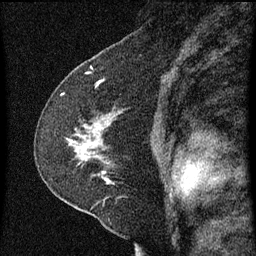
Breast MRI (dynamic contrast-enhanced), one sagittal slice. Slice 40 of 60 in the series (ordered by position). Dynamic contrast-enhanced series, image 2 of 3 at this slice position (ordered by acquisition). 1.5 T. TE 4.2 ms, TR 8 ms. 256 × 256 image matrix, field of view 180 × 180 mm. Patient: female, 47 years.
Structures marked on this image (semi-automatically segmented with operator editing):
- analysis volume of interest (the breast-tissue region the enhancement analysis was run in; not a lesion): bounding box (x1, y1, x2, y2) in pixels: (37, 98, 158, 213)
- tumour enhancement mask (voxels above the 70 % enhancement threshold inside the analysis volume of interest): (76, 134, 111, 183)